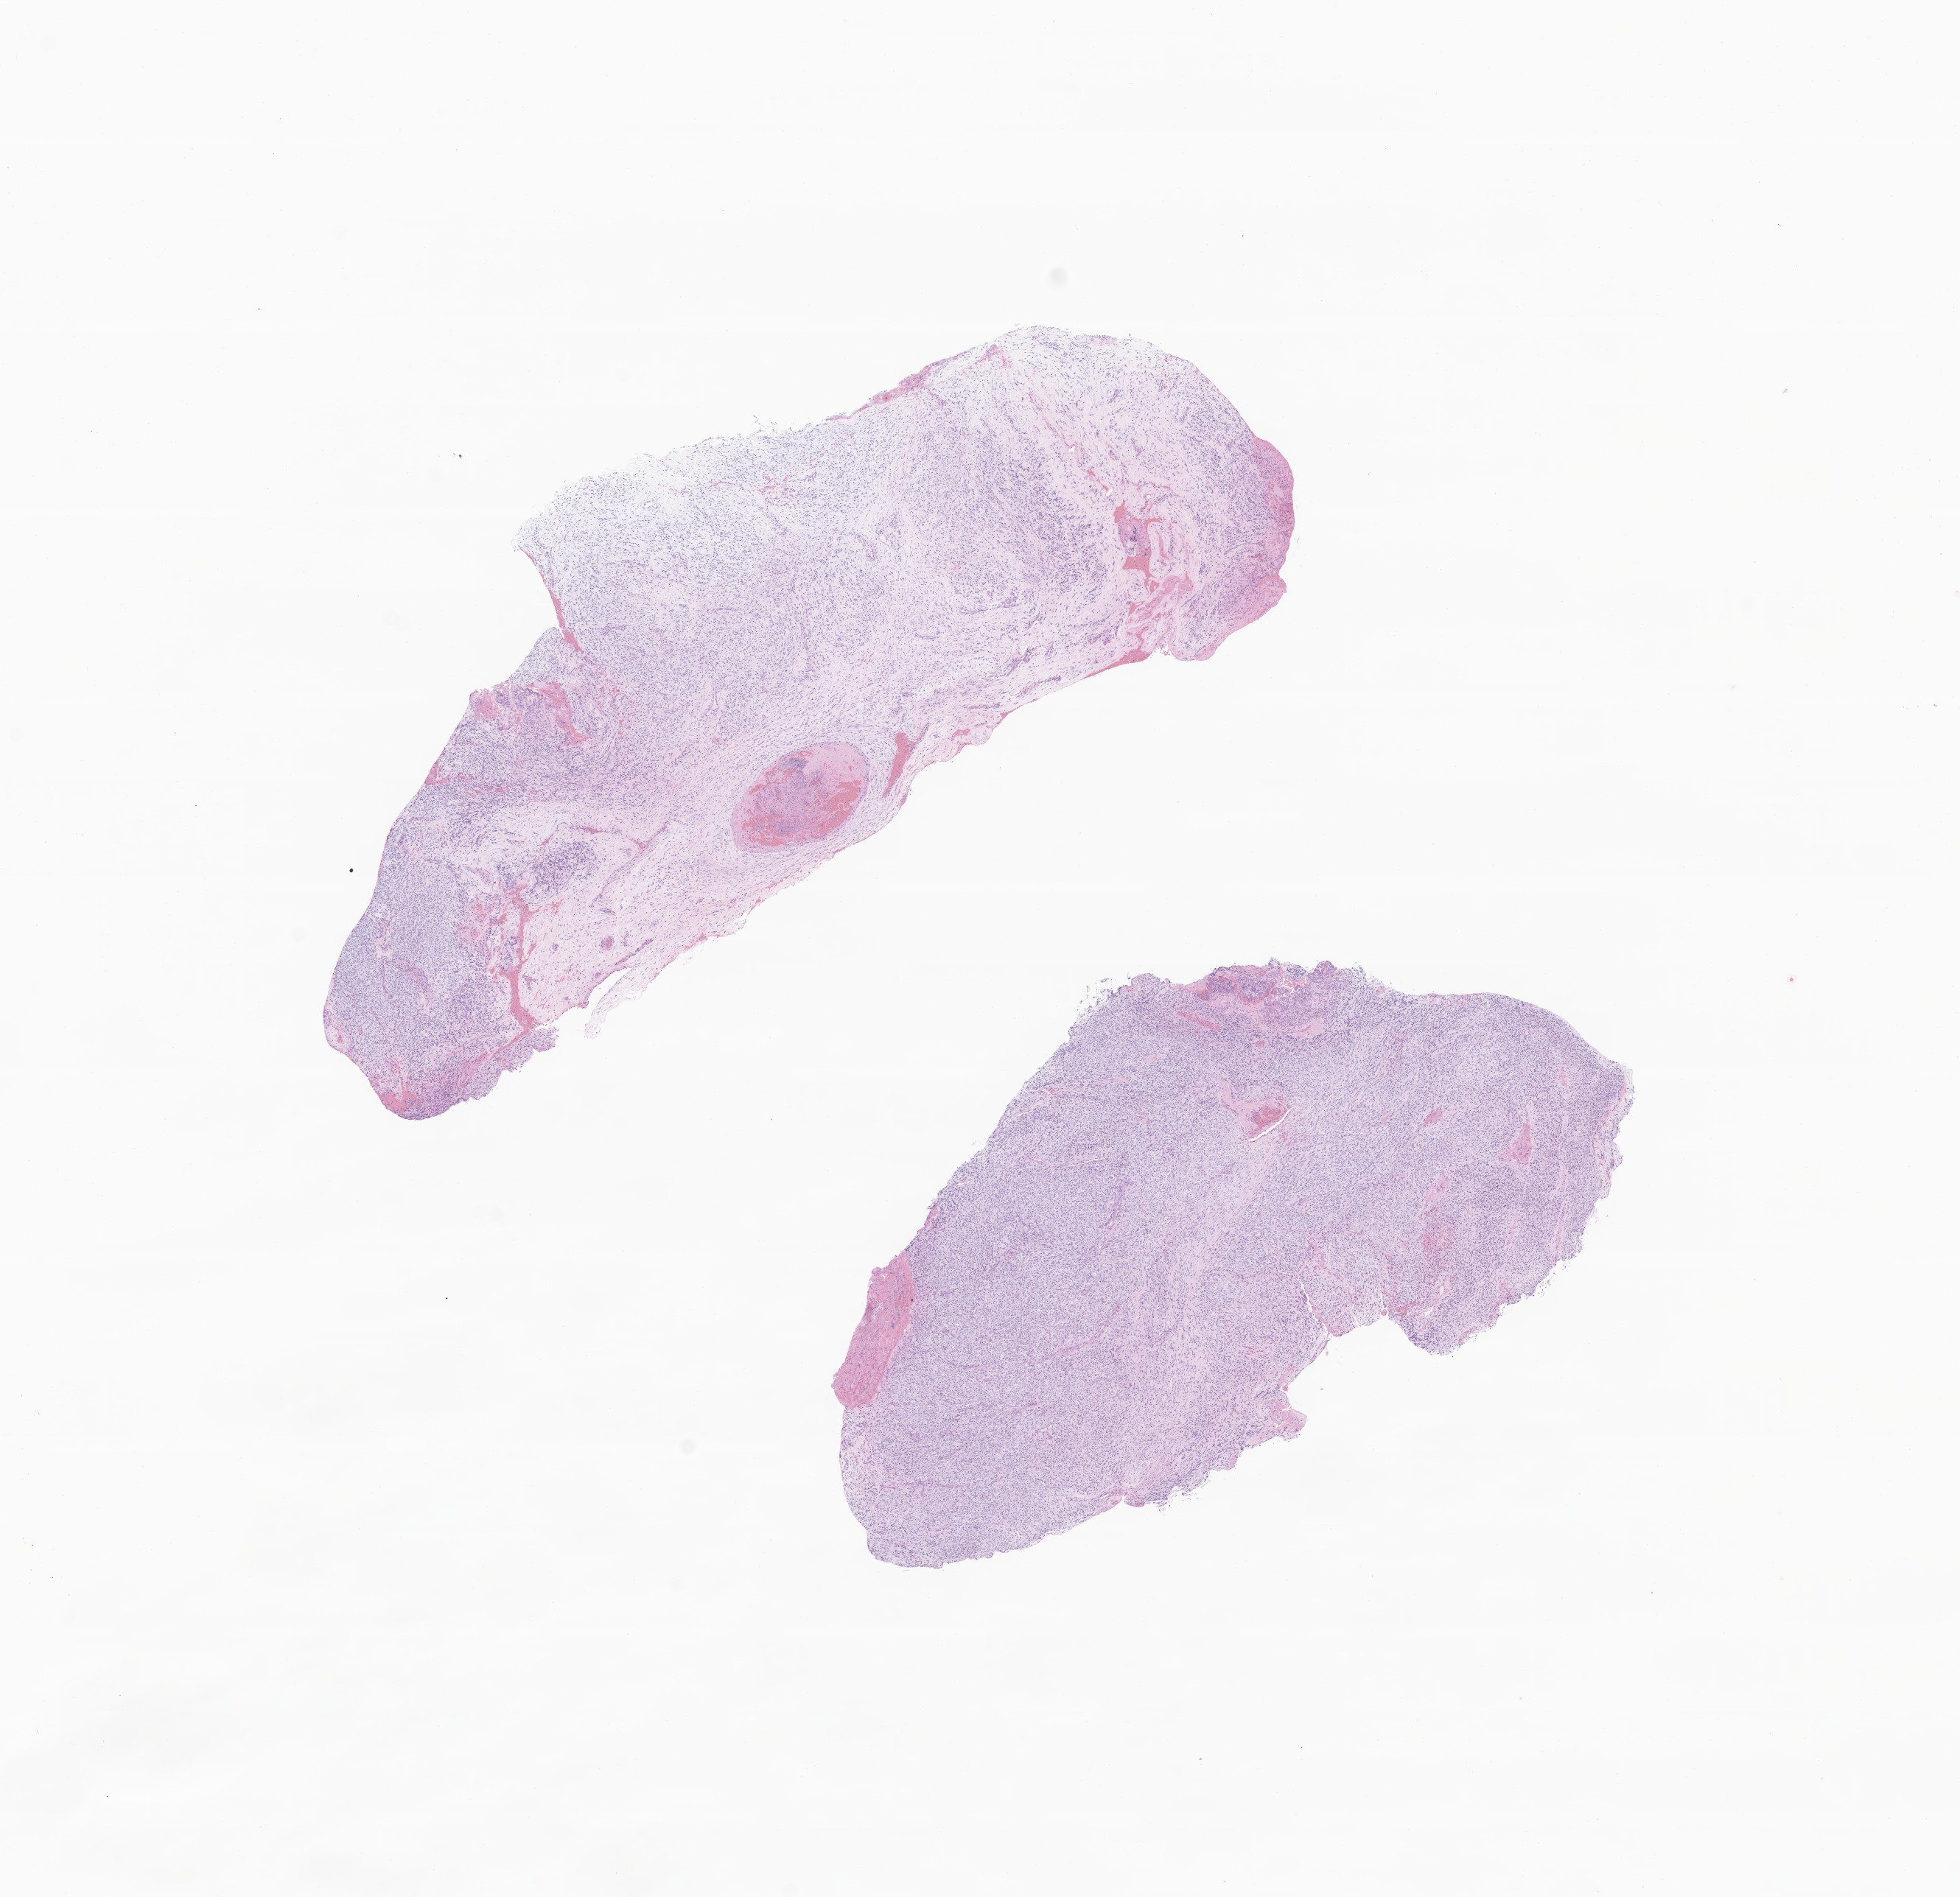
Digitized H&E-stained section of tumor tissue from the lower limb — shown as a low-resolution overview of the whole scanned area (about 11.2 x 10.9 mm). Formalin-fixed, paraffin-embedded (FFPE) tissue. Patient: female, age 18 days.
Recorded diagnosis: Spindle cell sarcoma.